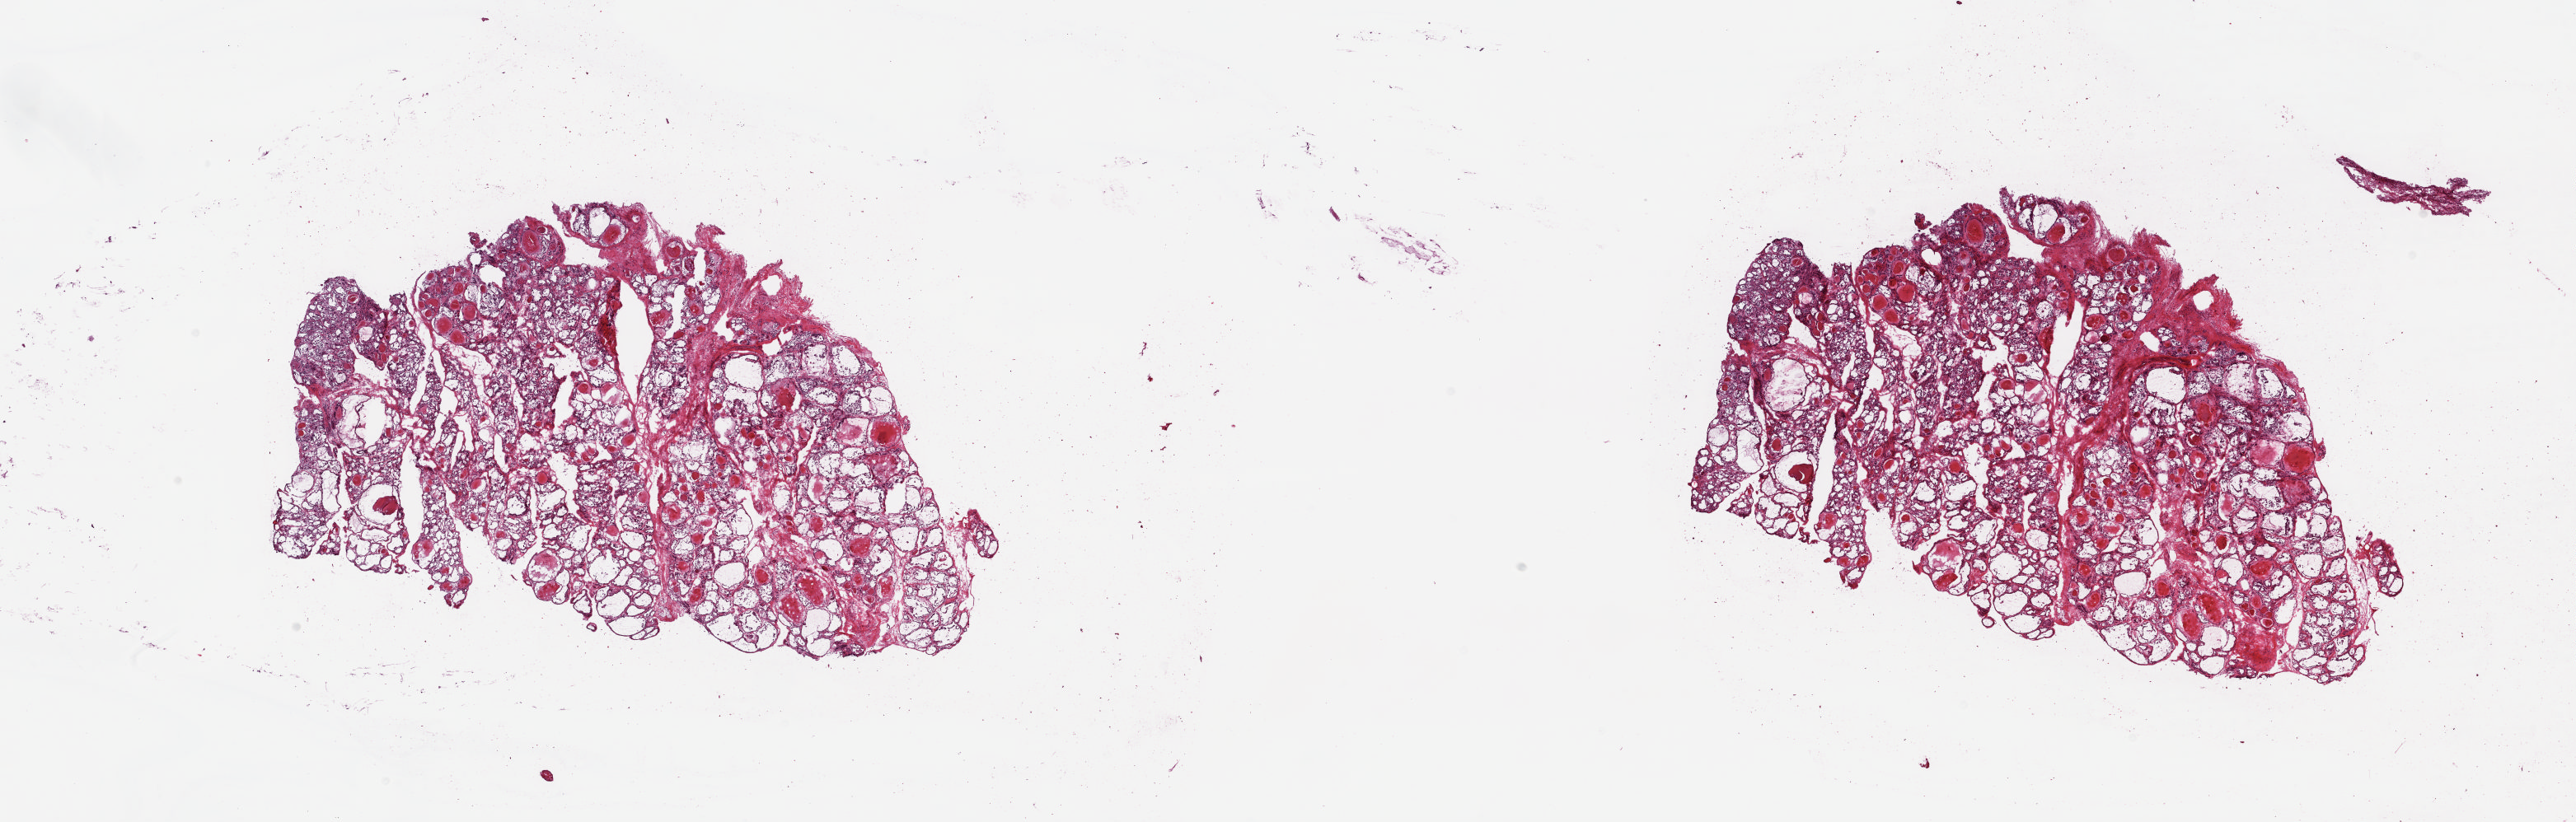
Whole-slide histology image, Hematoxylin and eosin (H&E) stained — low-resolution overview of the scanned area, about 24.8 x 7.9 mm (acquisition: 20x scan); frozen section from the top of the tissue portion; sample: solid tissue normal (non-tumour tissue), thyroid. Patient: female, age at initial diagnosis 55 years. Pathologist review of this section (percent, as recorded): tumour cells 0%, tumour nuclei 0%, normal cells 100%, stromal cells 0%, necrosis 0%. Infiltration values recorded for this section: lymphocyte infiltration 0%, monocyte infiltration 0%, neutrophil infiltration 0%.
This section: solid tissue normal (non-tumour) sample from the same patient. Patient diagnosis: Papillary adenocarcinoma, NOS.